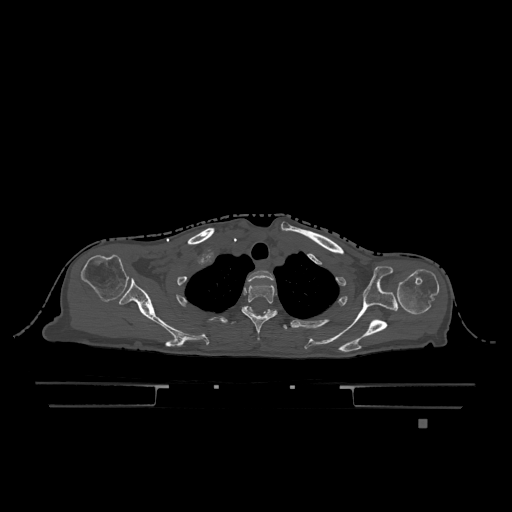
CT including the spine, one axial slice. Slice 958 of 1317 in the series (ordered by position). Bone window (W 1800 / L 400 HU). 0.5 mm slice thickness. 512 × 512 image matrix, field of view 500 × 500 mm. Female patient, age 74 years. Case-level facts recorded for this patient, not image findings: primary cancer: lung.
Annotated regions visible in this slice (semi-automatically segmented with operator editing):
- T1 vertebra: bounding box <248,270,274,282> (left, top, right, bottom; pixels)
- T2 vertebra: <241,283,278,340>
- T3 vertebra: <231,306,287,329>
- T6 vertebra: <248,306,277,313>